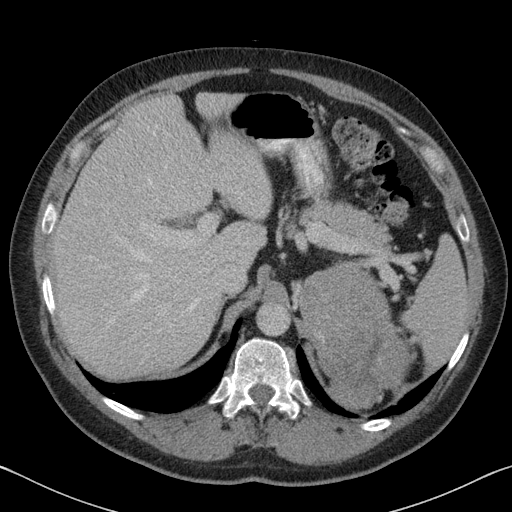
Contrast-enhanced abdominal CT, one axial slice; slice 59 of 88 in the series (ordered by position); reconstruction kernel B31f; soft-tissue window (W 400 / L 40 HU); 512 × 512 image matrix, field of view 366 × 366 mm. Patient: male, 51 years. From the clinical record (not read from this slice): diagnosis: adrenocortical carcinoma; tumour side: left adrenal; tumour size at pathology: 16.5 cm; Ki-67 index: 30 %; stage (as recorded): 2.
Structures marked on this image (semi-automatic segmentation, software-assisted and operator-edited):
- mass: bounding box <301,266,409,407> (left, top, right, bottom; pixels)